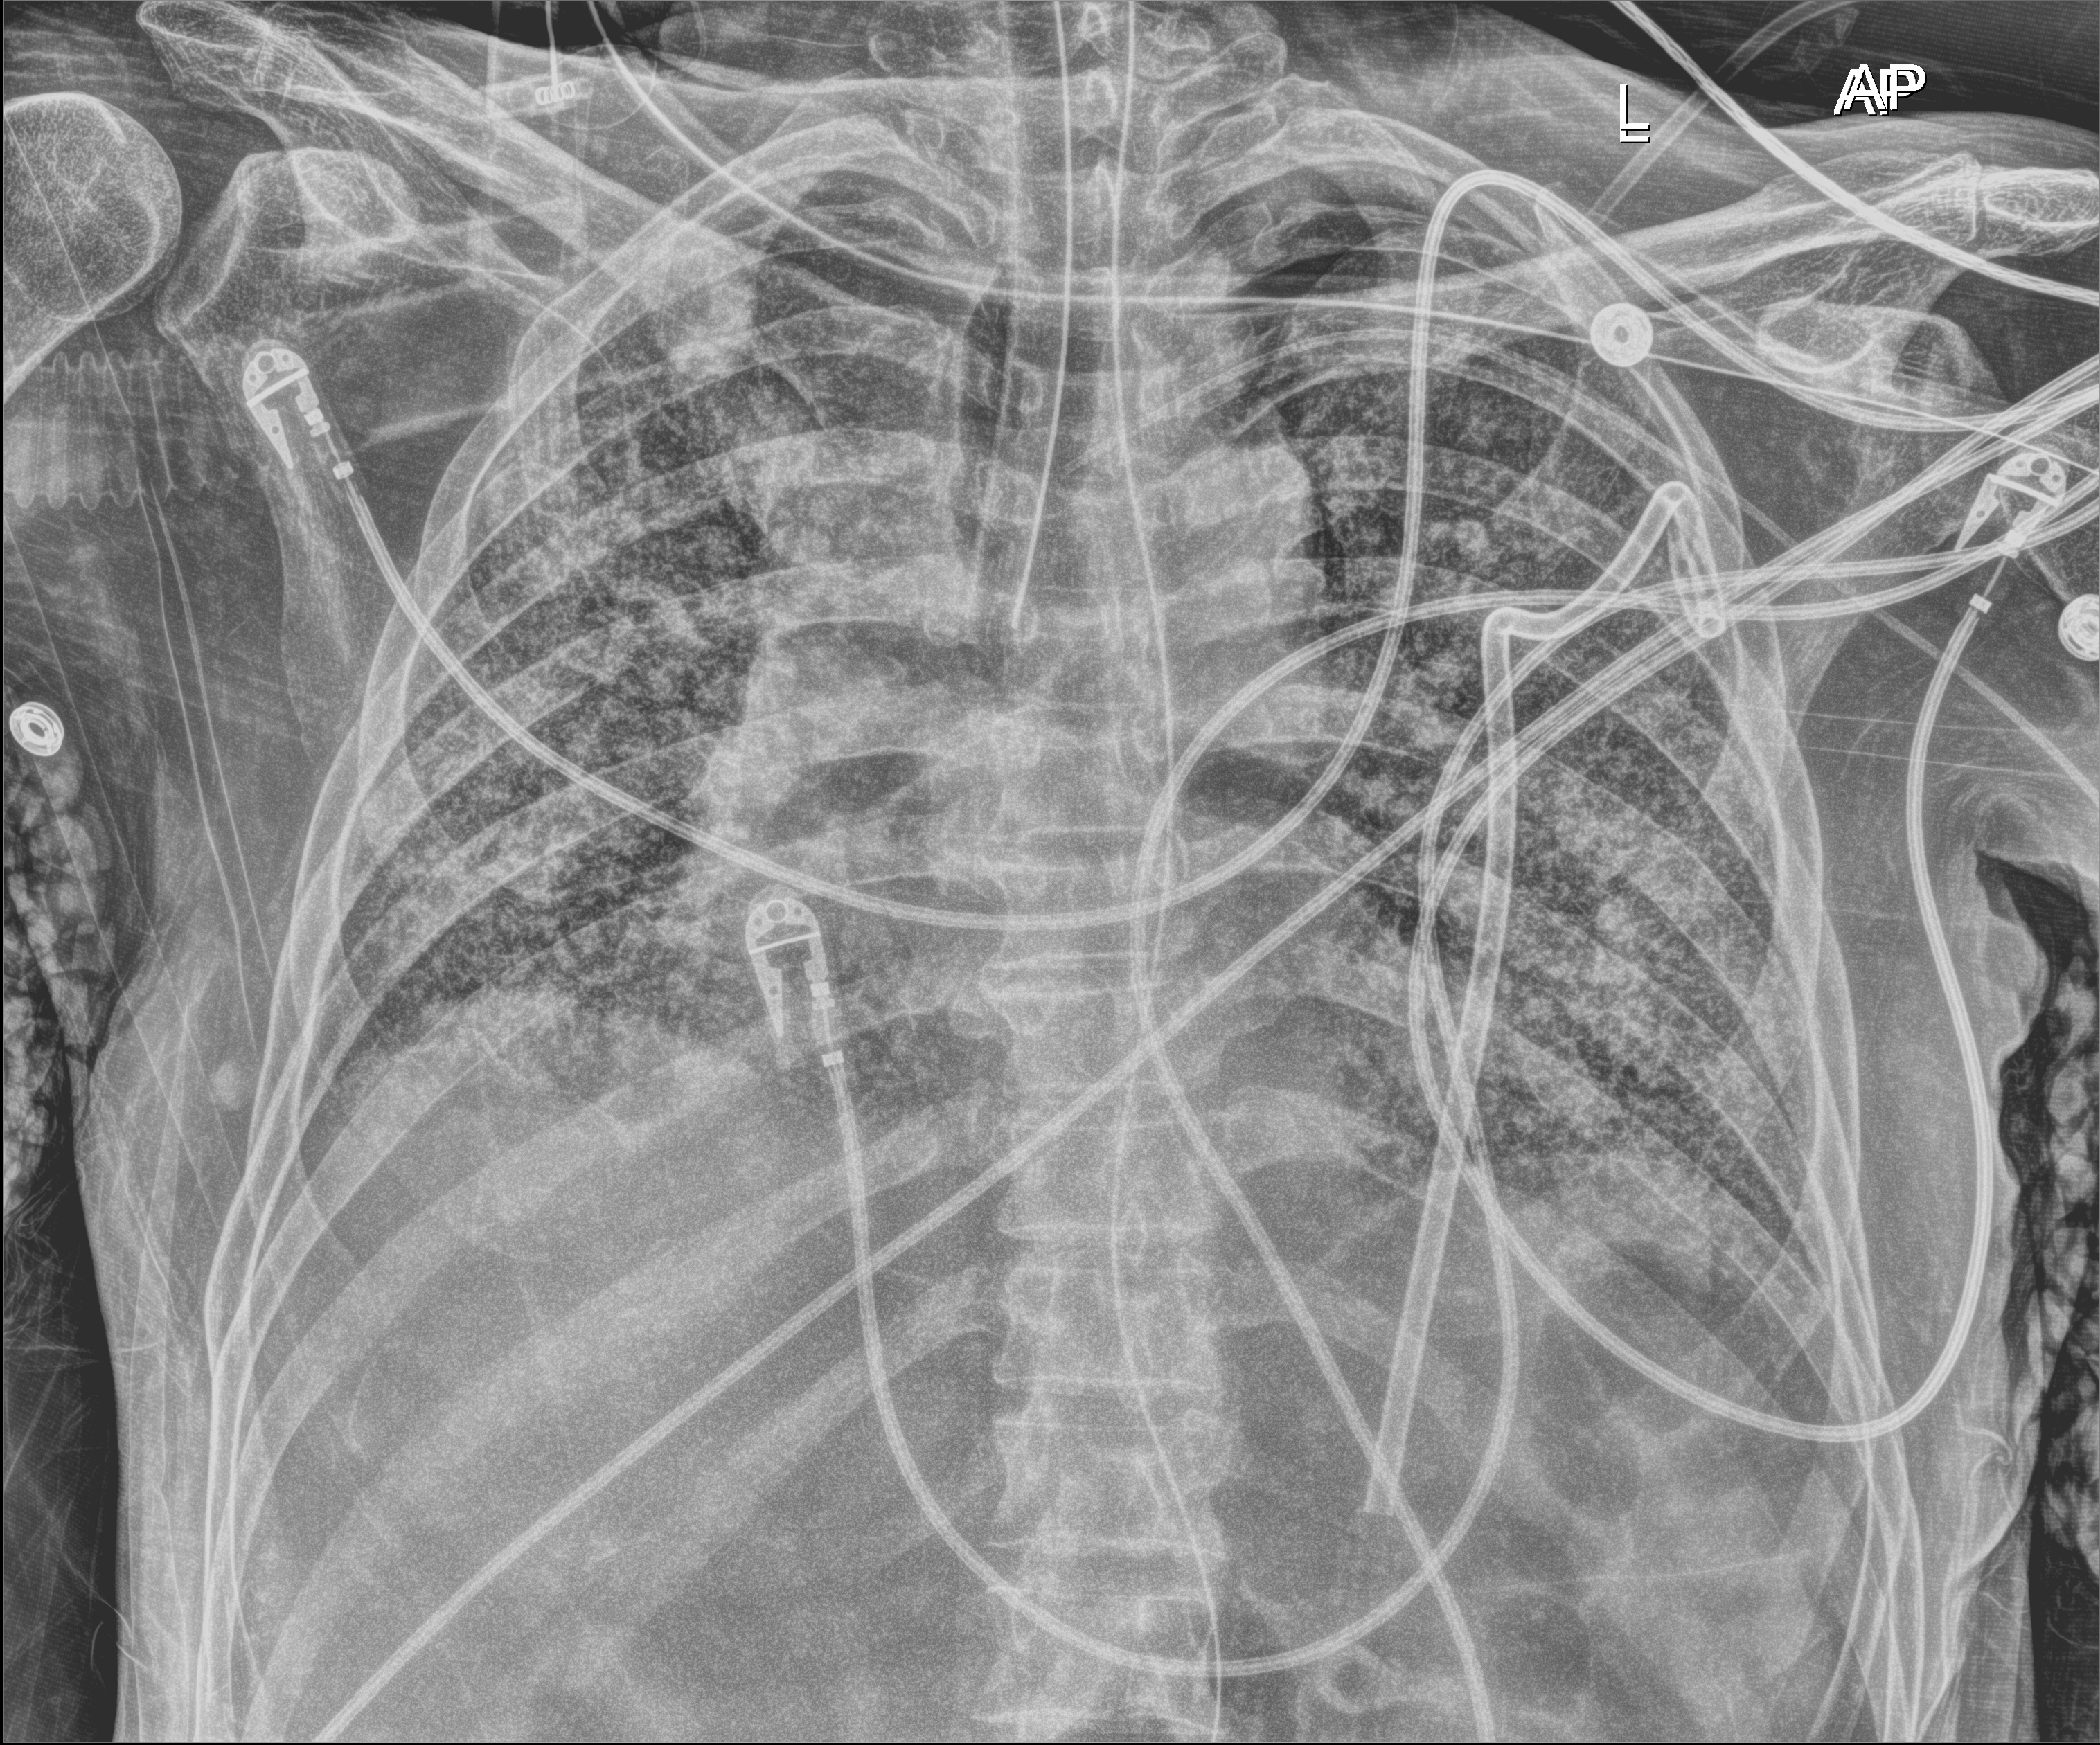
Portable chest radiograph; anteroposterior (AP) projection. Male patient hospitalised with COVID-19, age 60–74 years.
Admission-level facts for this patient (not findings on this image; timing relative to this image not recorded): admitted to intensive care during this hospital stay: yes; mechanically ventilated during this hospital stay: yes.